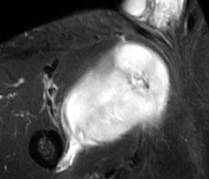
MRI of an extremity soft-tissue mass, one axial slice. Position 58 of 89 along the scan axis. STIR. MR volume resampled by the dataset authors to the PET/CT grid (not the native acquisition matrix). 209 × 179 image matrix. Male patient. From the clinical record (not read from this slice): histological type: undifferentiated - pleiomorphic; grade: high; site of the primary tumour: right thigh.
Outlined on this slice (expert contour drawn on MRI and transferred to this co-registered scan by the dataset authors):
- gross tumour volume including surrounding oedema: bounding box <60,41,170,149> (left, top, right, bottom; pixels)
- gross tumour volume (mass): <60,41,170,149>